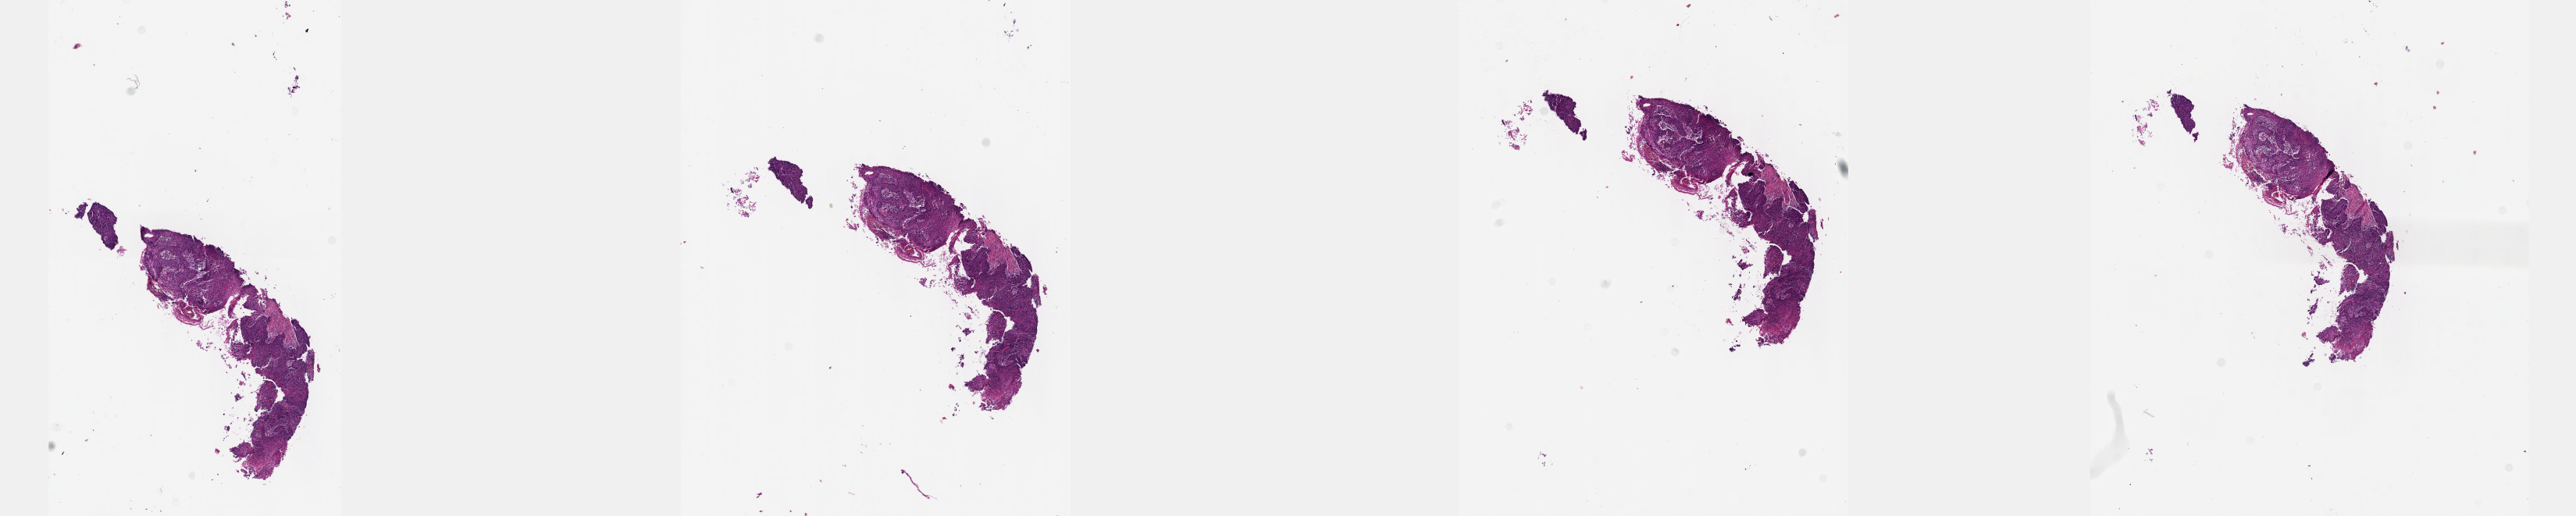
Whole-slide histology image, H&E-stained, a low-resolution overview of the entire scanned area, about 26.7 x 5.3 mm (acquisition: 40x scan). Formalin-fixed paraffin-embedded (FFPE) diagnostic section. Primary tumour sample from the esophagus. Male, age 67 years at initial diagnosis. Histologic grade: G3 (poorly differentiated).
Diagnosis: Squamous cell carcinoma, NOS. AJCC pathologic stage: IIB (7th edition).